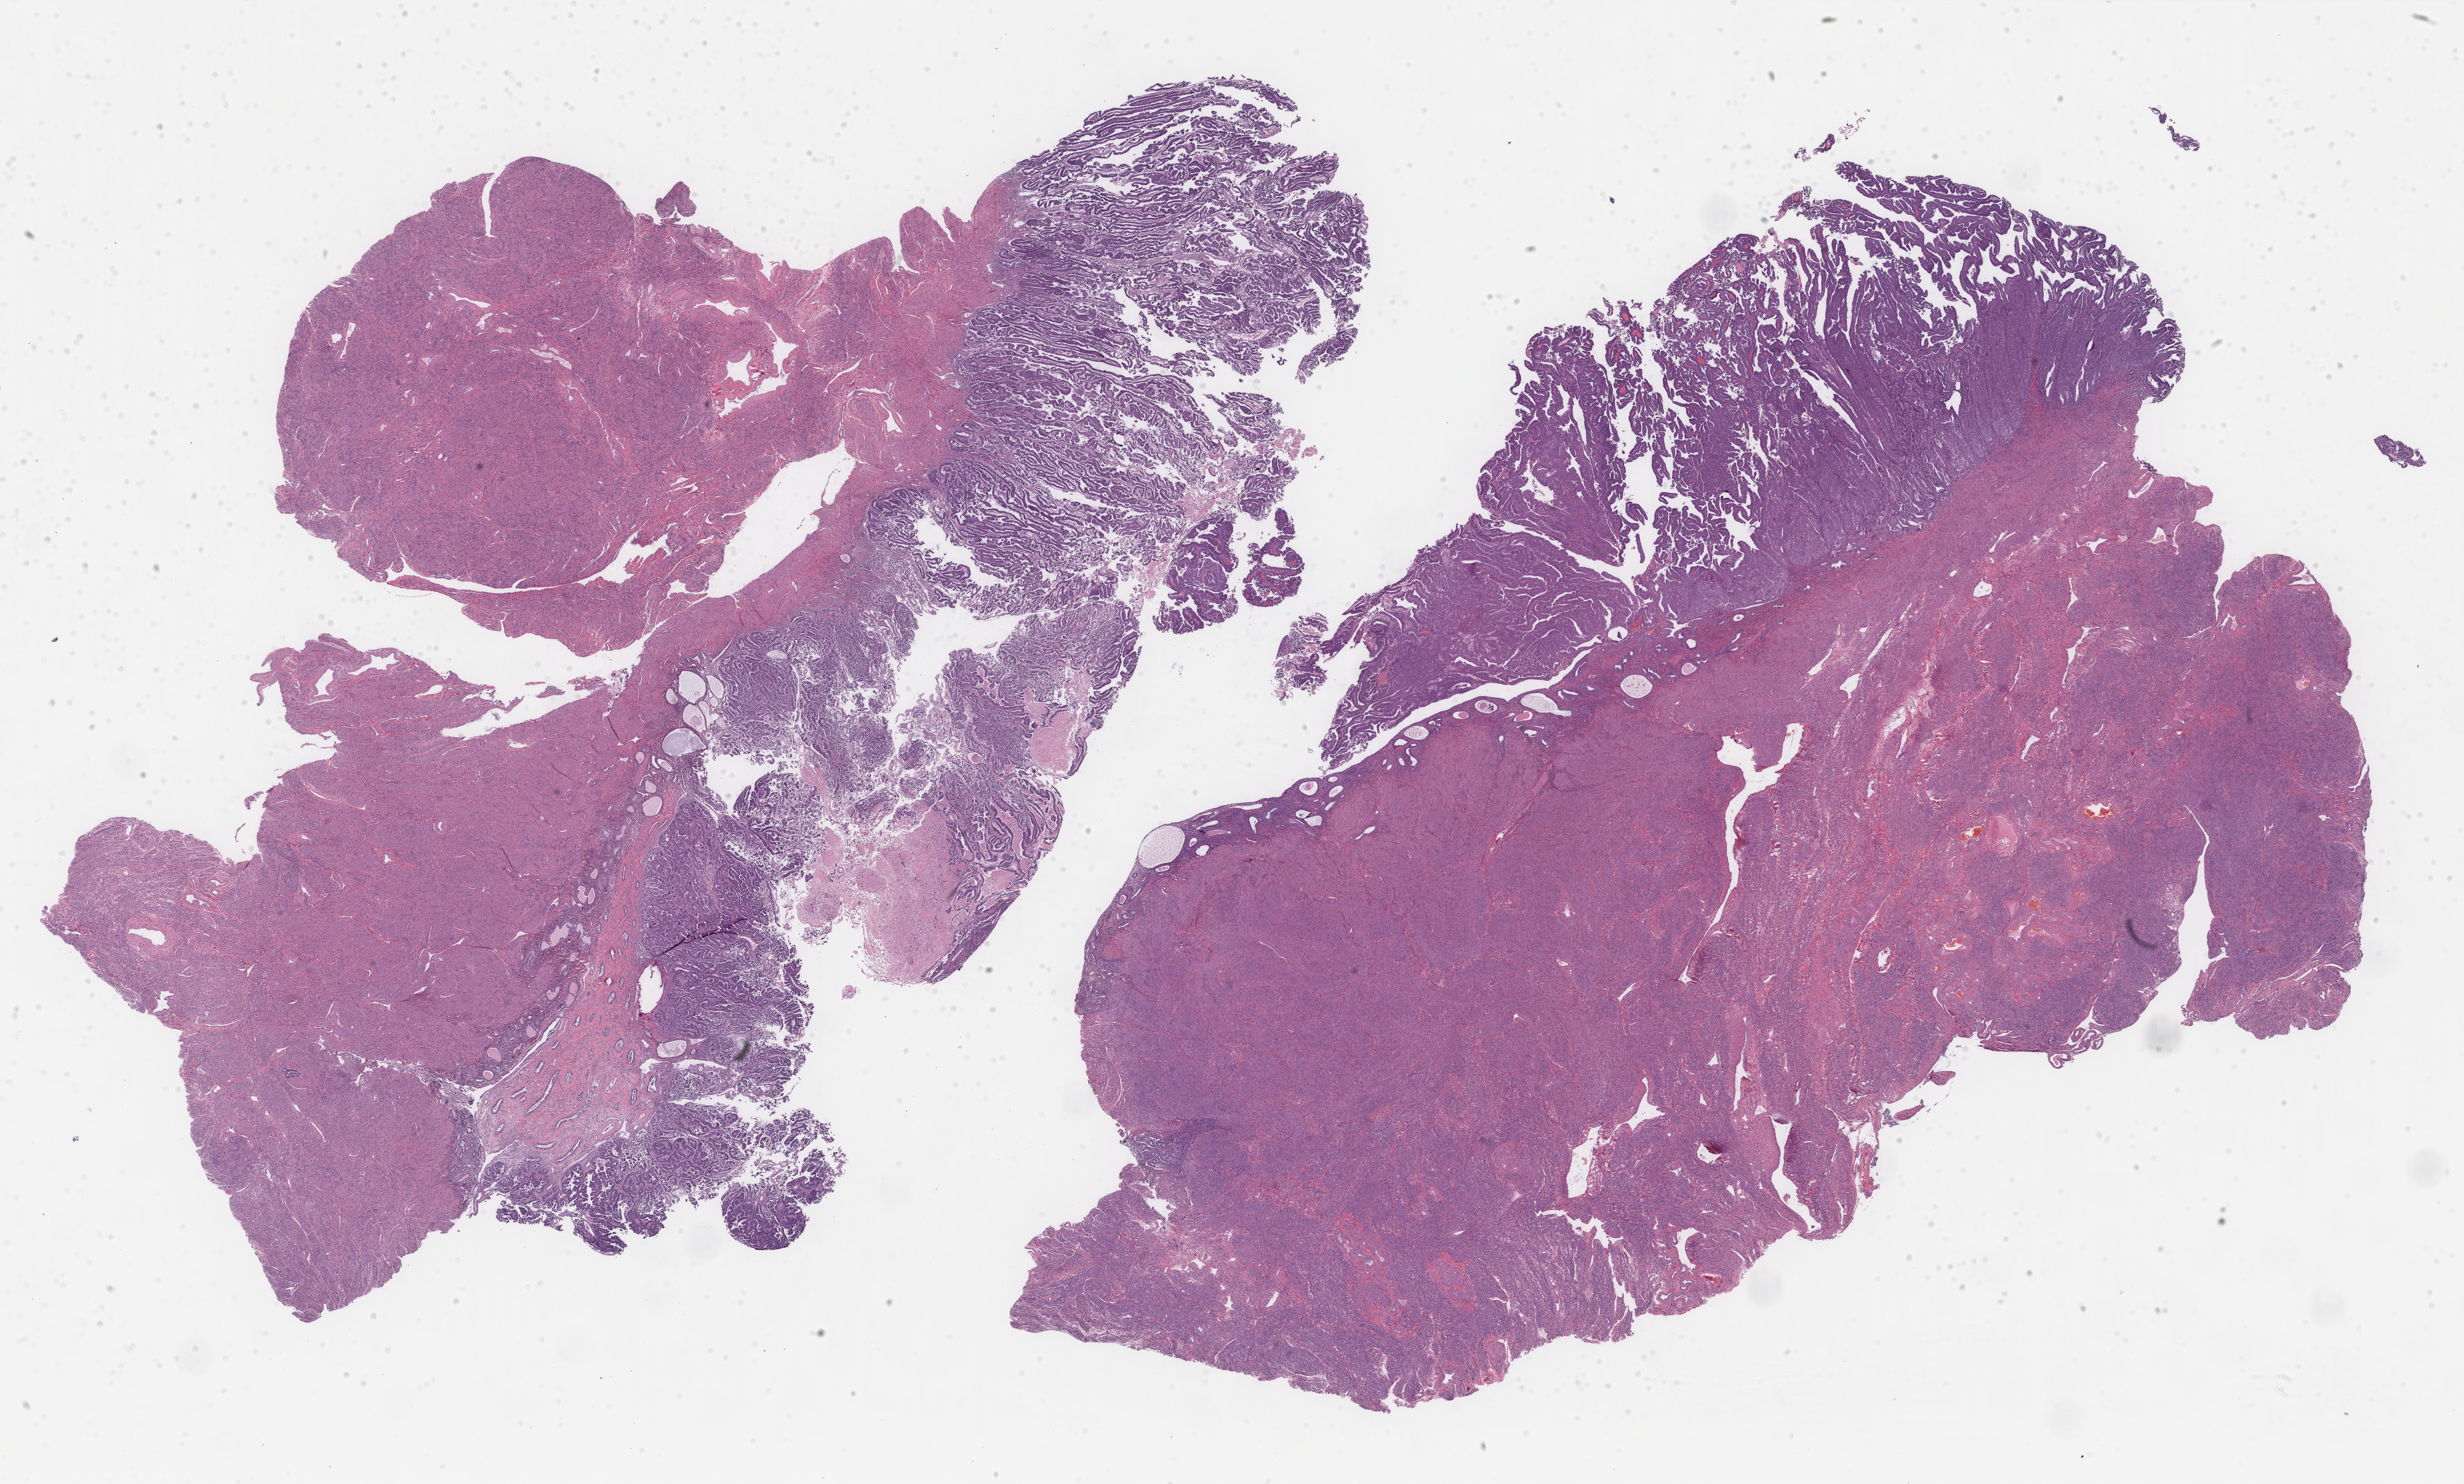
Digitized Hematoxylin and eosin (H&E) stained tissue section (whole slide), low-resolution overview of the scanned area, about 32.1 x 19.3 mm (acquisition: 40x scan). Formalin-fixed paraffin-embedded (FFPE) diagnostic section. Uterus, primary tumour sample. Female patient; age at initial diagnosis 74 years.
Histologic diagnosis: Serous cystadenocarcinoma, NOS (endometrium).